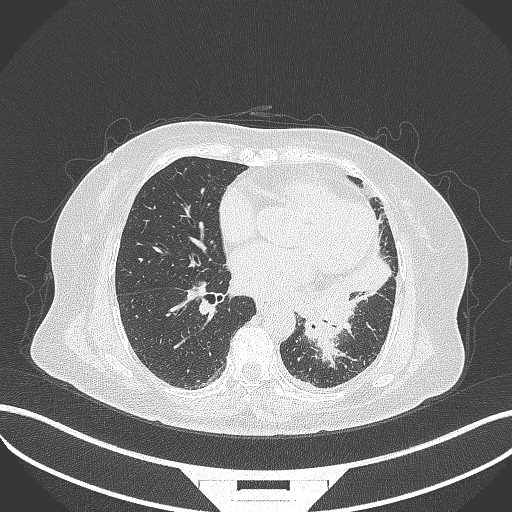
Chest CT, one axial slice. Slice 155 of 322 in the series (ordered by position). Lung window (W 1500 / L -600 HU). 512 × 512 image matrix, field of view 400 × 400 mm. Patient: female, 69 years. Case-level facts recorded for this patient, not image findings: clinical TNM (as recorded): T2b N3 M1.
Annotated regions visible in this slice (bounding box drawn by a radiologist):
- lung tumour (recorded histology: adenocarcinoma): box from (x=300, y=282) to (x=359, y=368) px